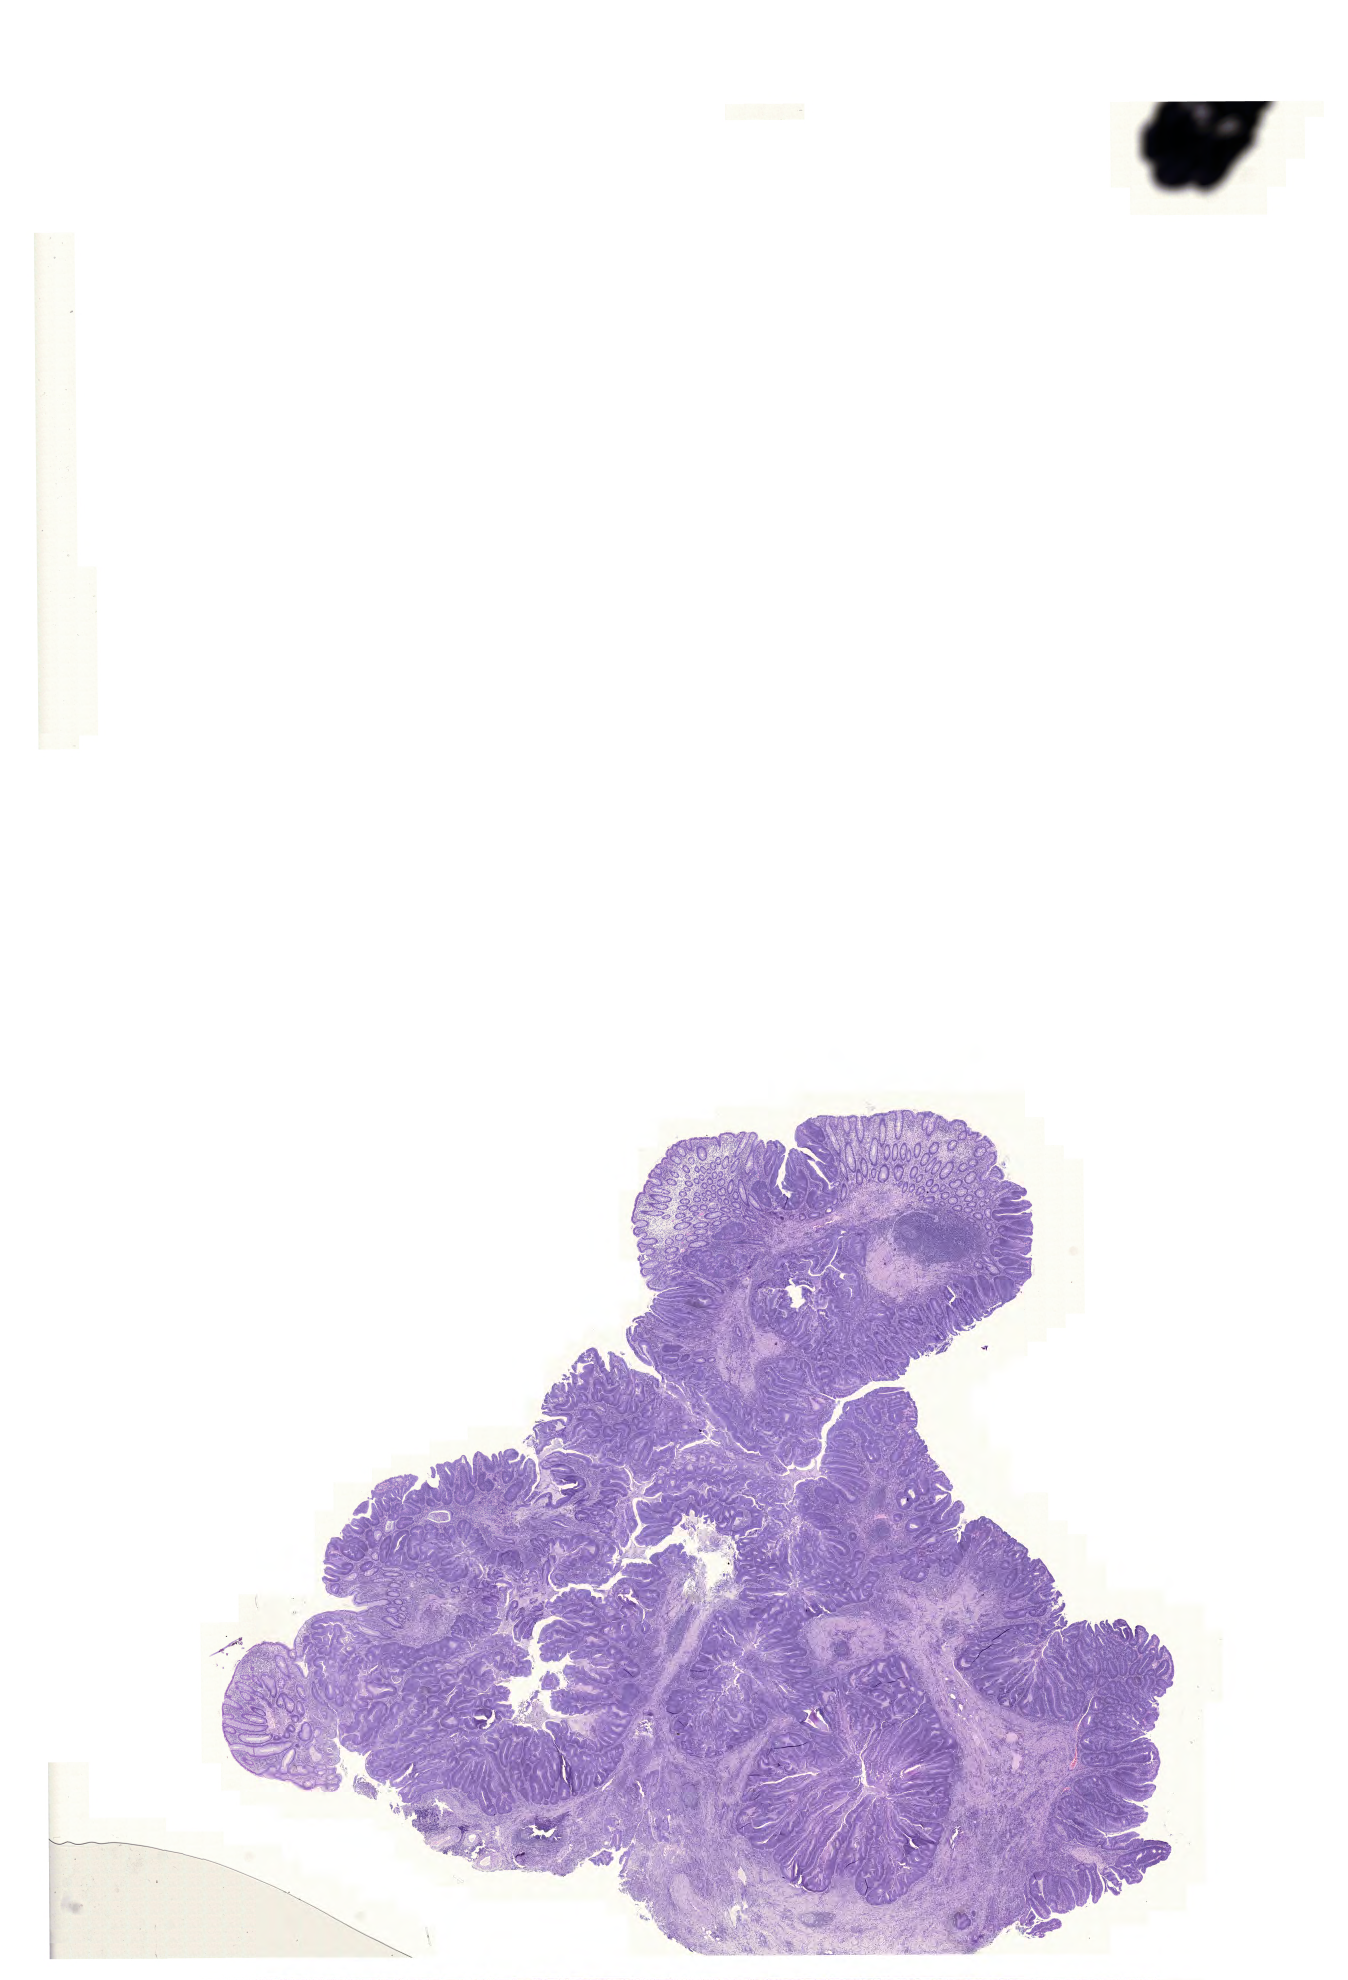
H&E whole-slide image — low-resolution overview of the scanned area, about 20.1 x 29.5 mm (from a 20x scan). Formalin-fixed paraffin-embedded (FFPE) diagnostic section. Colon, primary tumour sample. Patient: male, age at initial diagnosis 73 years.
* diagnosis: Adenocarcinoma, NOS
* lymph nodes positive (case pathology): 0 of 27 examined
* AJCC pathologic stage: I (5th edition)